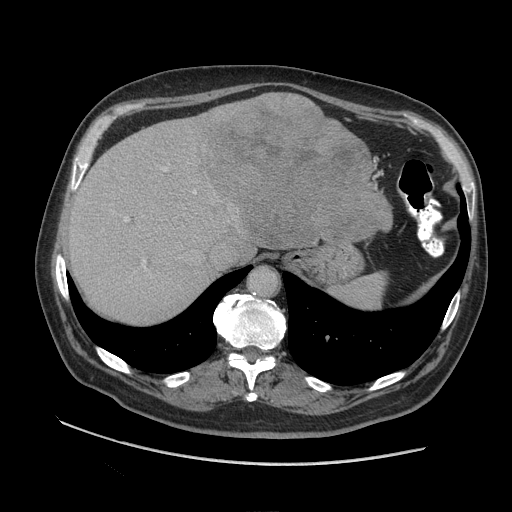
Contrast-enhanced abdominal CT (liver protocol), one axial slice; position 74 of 109 along the scan axis; reconstruction kernel STANDARD; 140 kVp; soft-tissue window (W 400 / L 40 HU); 2.5 mm slice thickness; 512 × 512 image matrix. Case-level facts recorded for this patient, not image findings: diagnosis: hepatocellular carcinoma (patient treated with transarterial chemoembolisation; whether this scan precedes or follows treatment is not stated here); TNM stage (as recorded): Stage-I; Child-Pugh class: A; tumour nodularity: uninodular.
Structures marked on this image (semi-automatically segmented with operator editing):
- abdominal aorta: bounding box <250,267,277,297> (left, top, right, bottom; pixels)
- liver parenchyma outside the tumour (the mass and vessels are separate outlines, so this box may not span the whole liver): <68,92,392,322>
- mass: <192,92,391,248>
- liver vessels: <124,167,196,269>